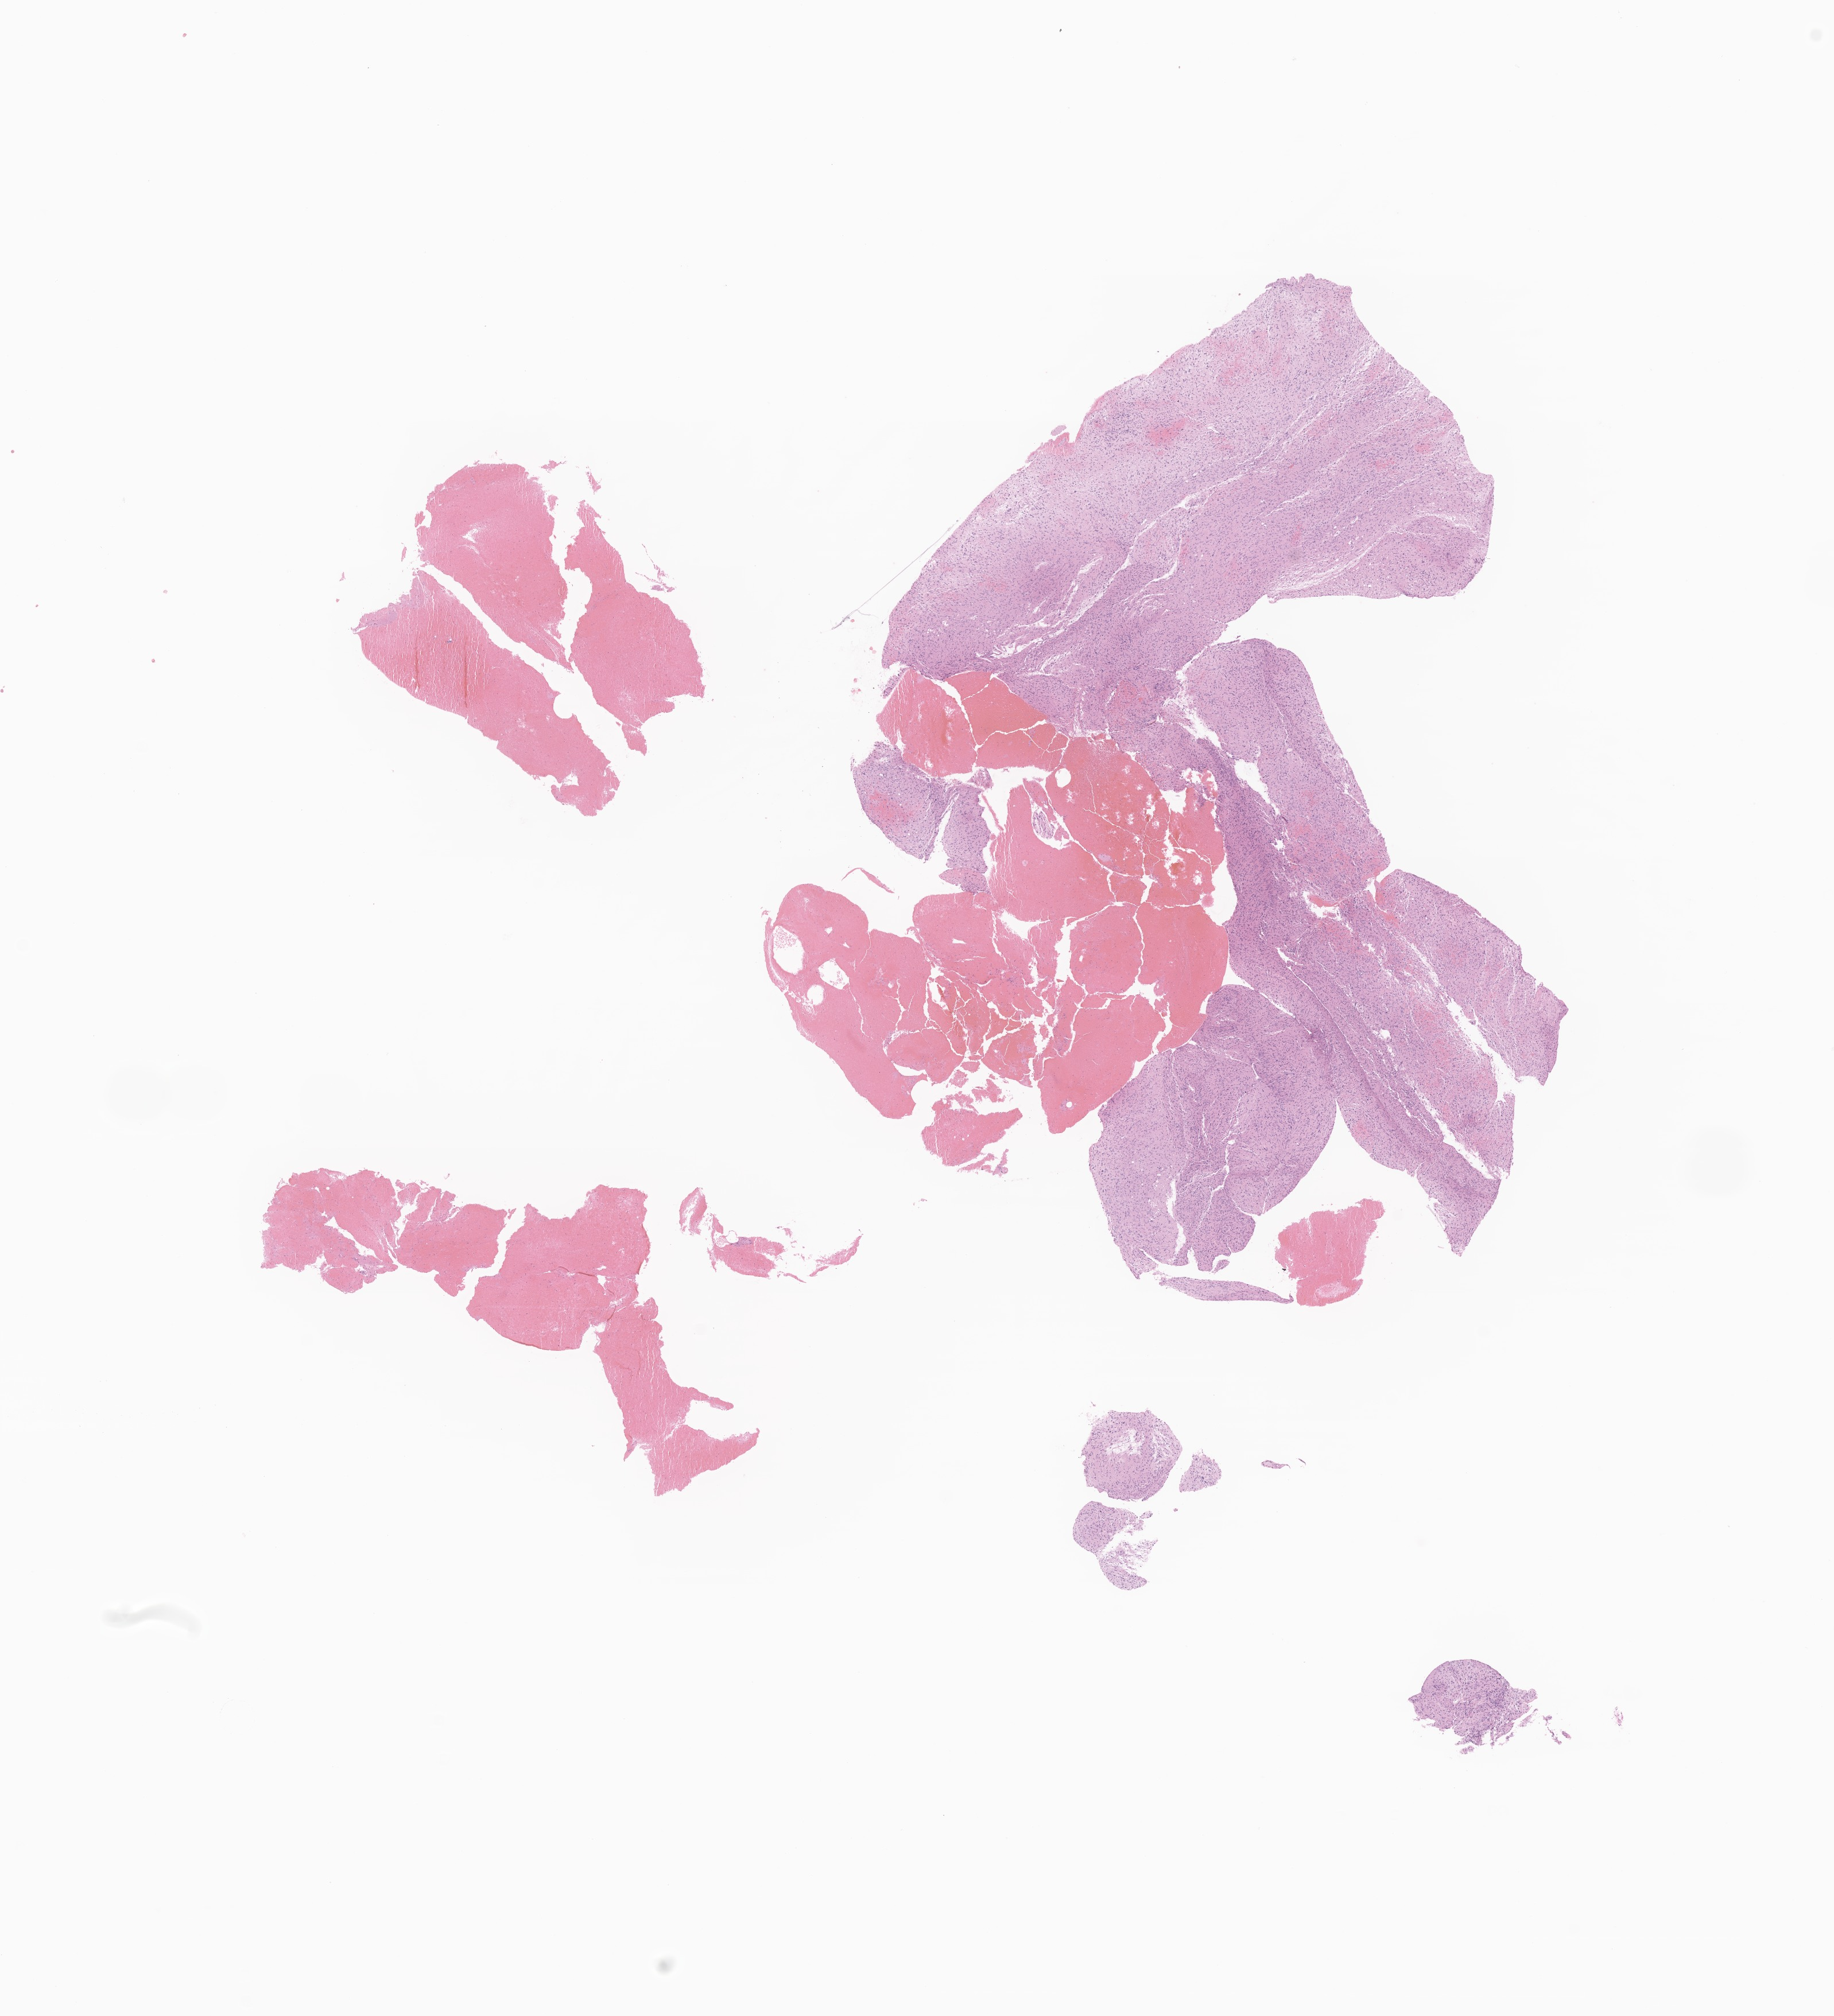
Digitized H&E-stained section of tumor tissue from the brain stem — shown as a low-resolution overview of the whole scanned area (about 13.5 x 14.8 mm), FFPE section. Patient female; age 125 months (10 years 5 months).
Recorded diagnosis: Glioma, malignant.